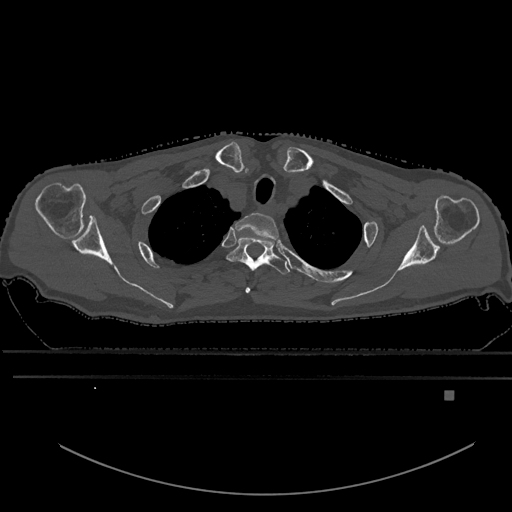
CT including the spine, one axial slice; bone window (W 1800 / L 400 HU); 0.5 mm slice thickness; 512 × 512 image matrix, field of view 456 × 456 mm. Male patient, age 82 years. From the clinical record (not read from this slice): primary cancer: prostate; vertebrae with lytic lesions (as recorded): T11, T9, T8, T2.
Outlined on this slice (semi-automatically segmented with operator editing):
- T1 vertebra: bounding box <235,212,279,293> (left, top, right, bottom; pixels)
- T2 vertebra: <227,237,290,294>